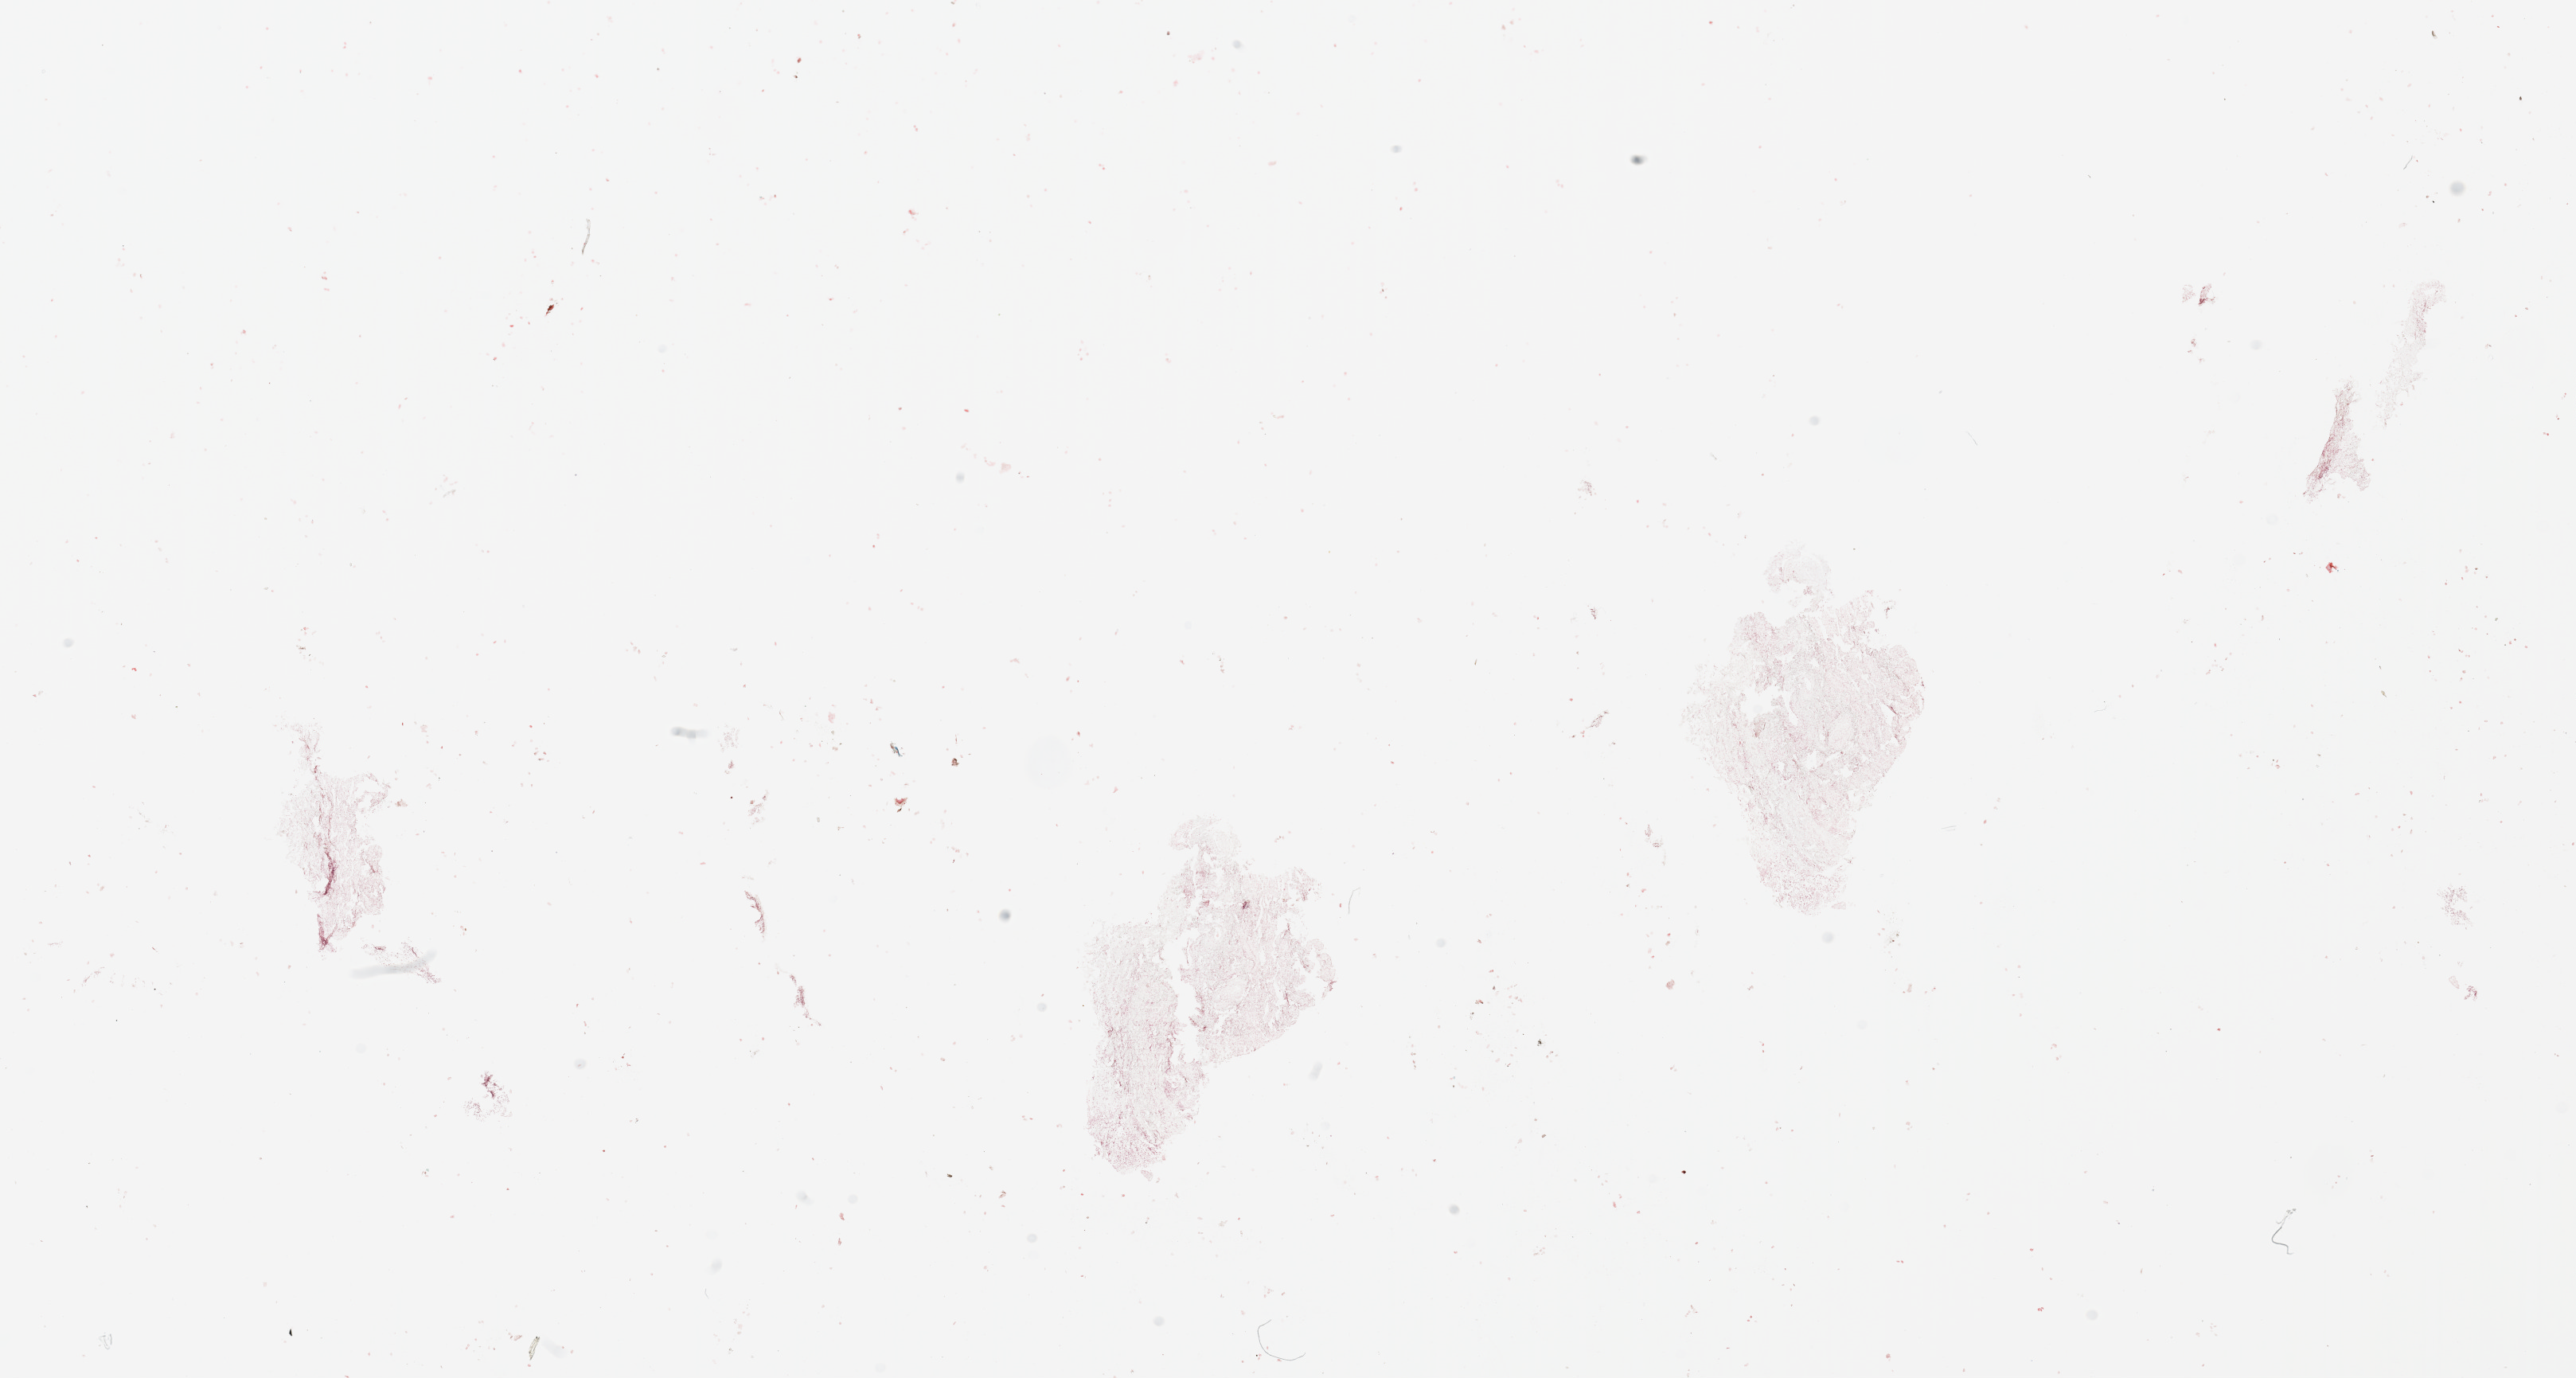
Hematoxylin and eosin (H&E) stained whole-slide image — a low-resolution overview of the entire scanned area, about 25.6 x 13.7 mm (from a 20x scan). Head and neck, tissue type not recorded. Male, 64 y/o.
- patient diagnosis: Squamous cell carcinoma, NOS (larynx, NOS)